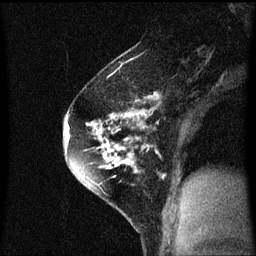
Breast MRI (dynamic contrast-enhanced), one sagittal slice. Position 39 of 60 along the scan axis. Dynamic contrast-enhanced series, image 2 of 3 at this slice position (ordered by acquisition). 1.5 T. TE 4.2 ms, TR 8.4 ms. 2 mm slice thickness. 256 × 256 image matrix. Female patient, age 60 years.
Outlined on this slice (semi-automatically segmented with operator editing):
- analysis volume of interest (the breast-tissue region the enhancement analysis was run in; not a lesion): bounding box (x1, y1, x2, y2) in pixels: (64, 70, 147, 195)
- tumour enhancement mask (voxels above the 70 % enhancement threshold inside the analysis volume of interest): (66, 108, 147, 187)